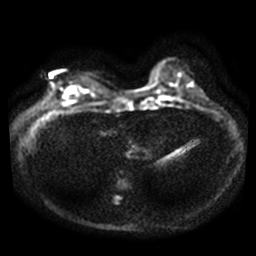
Breast MRI, one axial slice; position 8 of 40 along the scan axis; diffusion-weighted series; image 2 of 4 stored at this slice position (different b-values; order by instance number); 3 T; 5 mm slice thickness; 256 × 256 image matrix. Female patient.
Structures marked on this image (outlined manually by an expert reader):
- tumour on diffusion-weighted imaging: bounding box <63,89,76,98> (left, top, right, bottom; pixels)